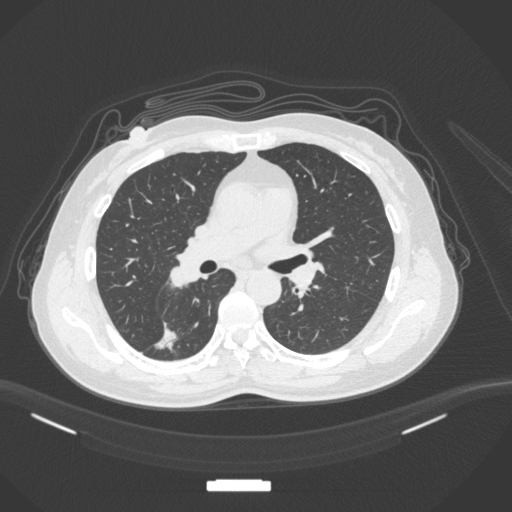
Chest CT, one axial slice; slice 174 of 352 in the series (ordered by position); reconstruction kernel B31f; lung window (W 1500 / L -600 HU); 512 × 512 image matrix, field of view 400 × 400 mm. Female patient, age 55 years. Case-level facts recorded for this patient, not image findings: clinical TNM (as recorded): T1c N1 M0.
Outlined on this slice (rectangle marked by the reading radiologist):
- lung tumour (recorded histology: adenocarcinoma): box from (x=150, y=325) to (x=184, y=353) px